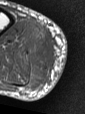
MRI of an extremity soft-tissue mass, one axial slice. Slice 12 of 47 in the series (ordered by position). MR volume resampled by the dataset authors to the PET/CT grid (not the native acquisition matrix). 3.27 mm slice thickness. 85 × 114 image matrix, field of view 83 × 111 mm. Male patient. From the clinical record (not read from this slice): histological type: pleiomorphic liposarcoma; grade: high; site of the primary tumour: right calf.
Annotated regions visible in this slice (expert contour drawn on MRI and transferred to this co-registered scan by the dataset authors):
- gross tumour volume including surrounding oedema: bounding box (x1, y1, x2, y2) in pixels: (27, 34, 55, 76)
- gross tumour volume (mass): (42, 53, 44, 56)